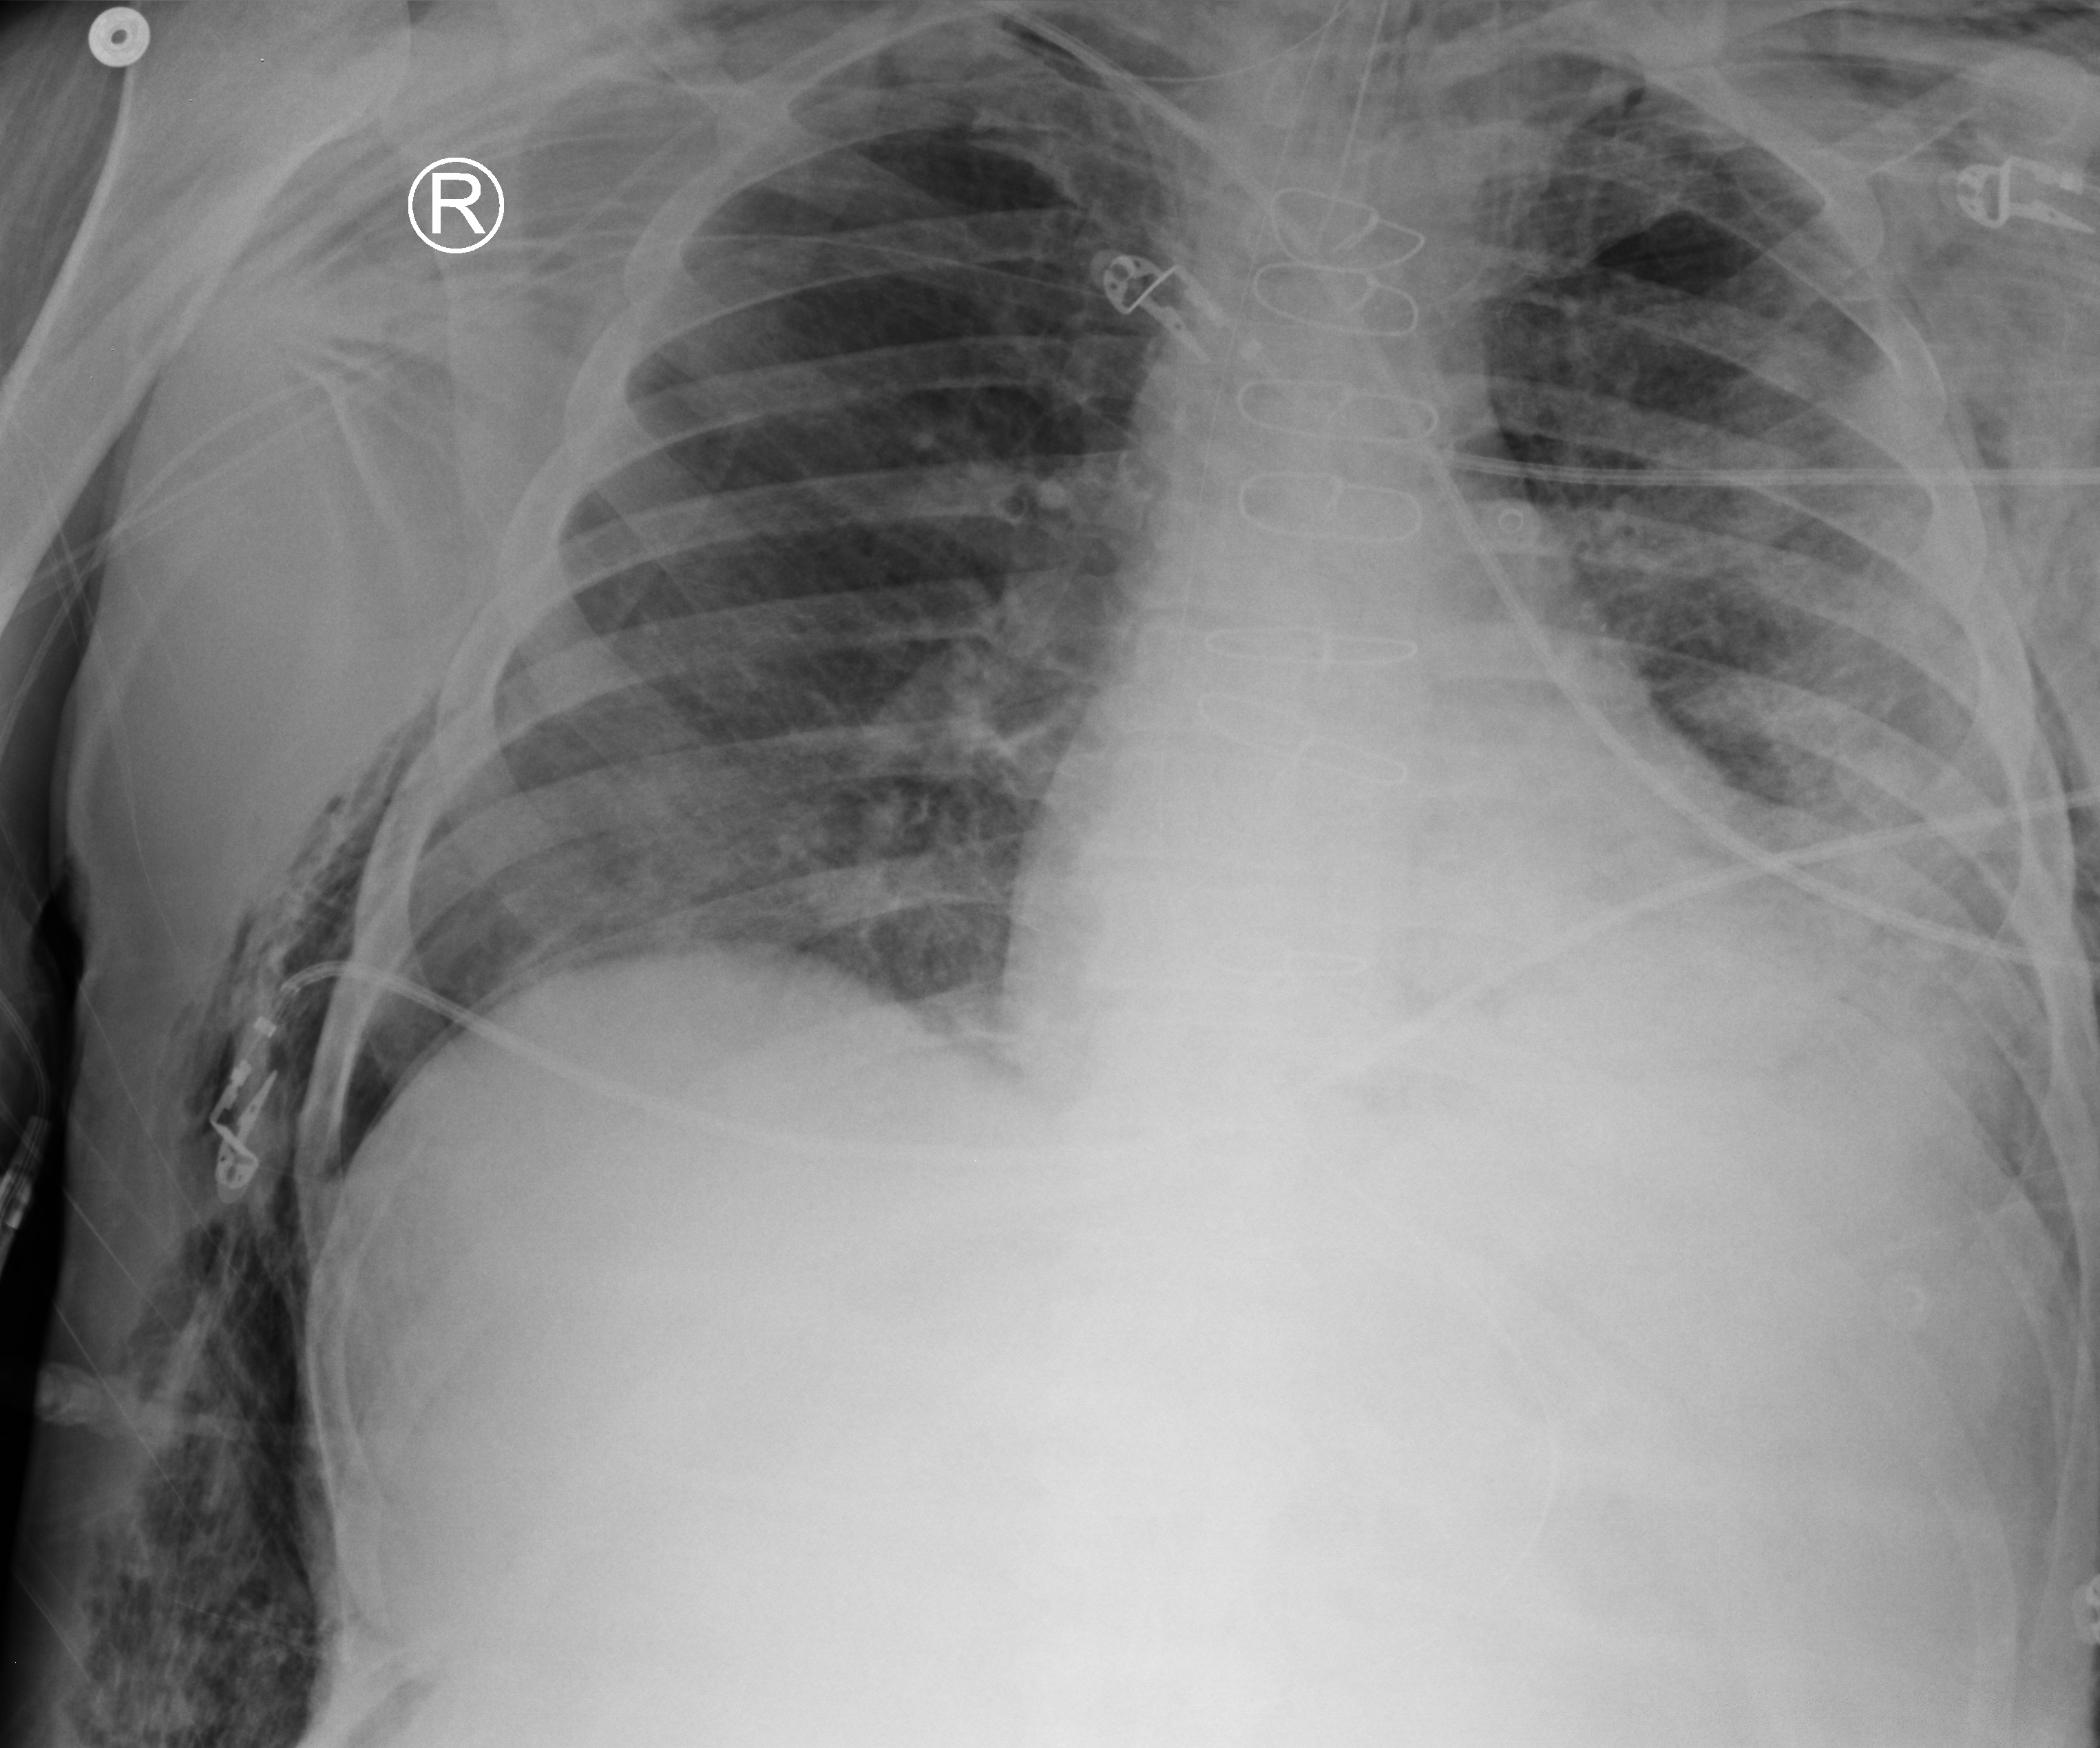
Bedside chest radiograph (computed radiography); anteroposterior (AP) projection. Male patient hospitalised with COVID-19, age 60–74 years.
Admission-level facts for this patient (not findings on this image; timing relative to this image not recorded): diabetes (admission record): yes; admitted to intensive care during this hospital stay: yes.